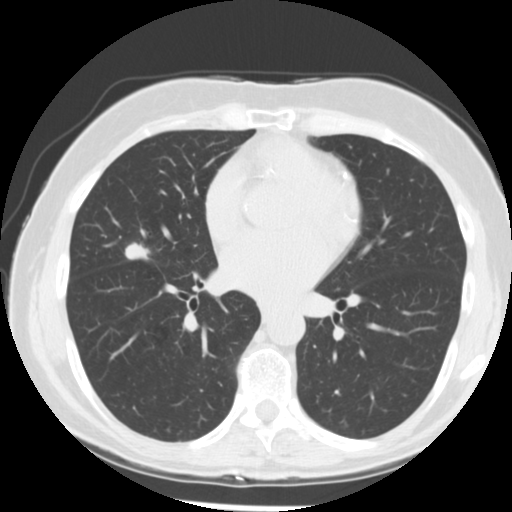
Low-dose screening chest CT, one axial slice. Slice 131 of 255 in the series (ordered by position). Reconstruction kernel STANDARD. Lung window (W 1500 / L -600 HU). 2.5 mm slice thickness. 512 × 512 image matrix, field of view 320 × 320 mm.
Structures marked on this image (manually delineated by an expert):
- lesion 1 (tumor, middle lobe of right lung): bounding box (x1, y1, x2, y2) in pixels: (125, 242, 150, 260)